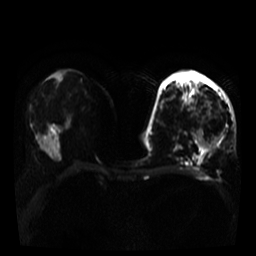
Breast MRI, one axial slice. Slice 16 of 35 in the series (ordered by position). Diffusion-weighted series; image 2 of 4 stored at this slice position (different b-values; order by instance number). 3 T. 256 × 256 image matrix. Female patient.
Annotated regions visible in this slice (expert manual segmentation):
- tumour on diffusion-weighted imaging: bounding box [x1, y1, x2, y2] px = [197, 135, 222, 149]